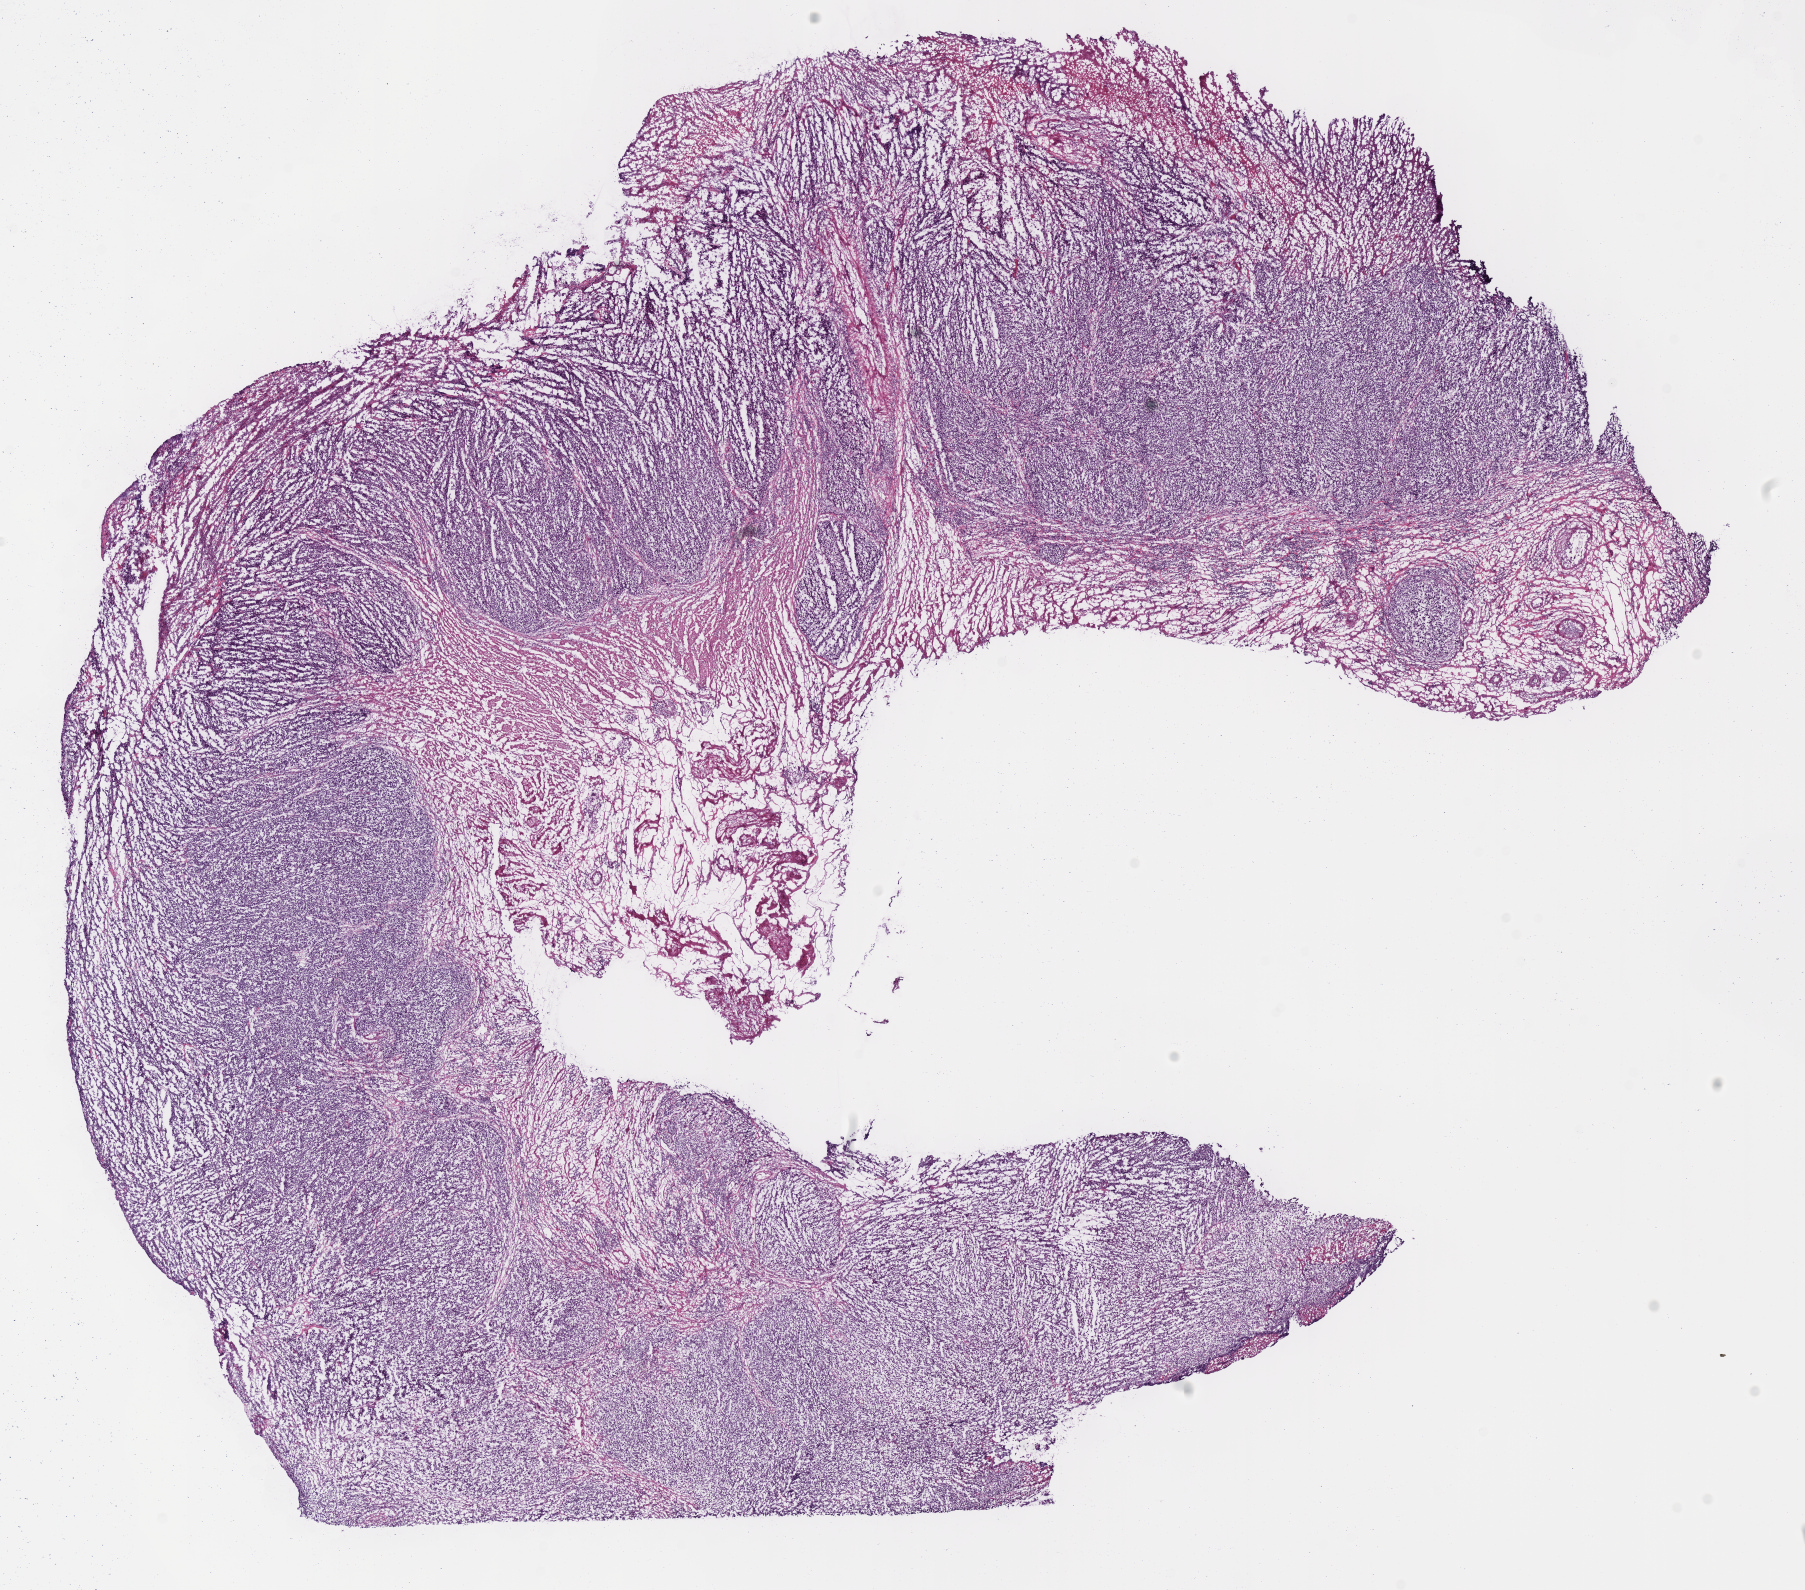
Digitized H&E-stained tissue section (whole slide) — low-resolution overview of the scanned area, about 14.2 x 12.5 mm; frozen section from the top of the tissue portion; stomach, primary tumour sample. Female, age 75 years at initial diagnosis. Histologic grade: G3 (poorly differentiated). Pathologist review of this section (percent, as recorded): tumour cells 80%, tumour nuclei 90%, normal cells 5%, stromal cells 13%, necrosis 2%. Infiltration values recorded for this section: lymphocyte infiltration 2%.
Histologic diagnosis: Adenocarcinoma, NOS (cardia, NOS). AJCC pathologic stage: IIB (7th edition).